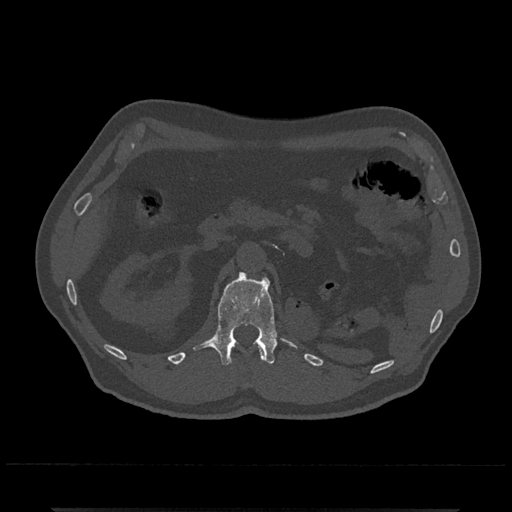
CT including the spine, one axial slice; slice 373 of 797 in the series (ordered by position); reconstruction kernel Br40s/3; 120 kVp; bone window (W 1800 / L 400 HU); 0.5 mm slice thickness; 512 × 512 image matrix. Male patient, age 67 years. Case-level facts recorded for this patient, not image findings: primary cancer: prostate.
Structures marked on this image (semi-automatic segmentation, software-assisted and operator-edited):
- L1 vertebra: bounding box <192,271,299,365> (left, top, right, bottom; pixels)
- T12 vertebra: <257,343,266,359>